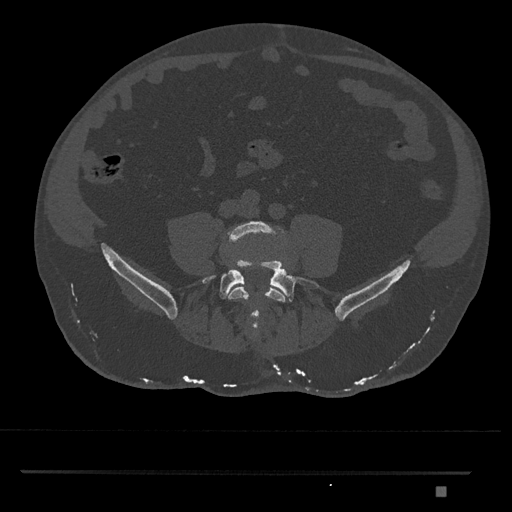
CT including the spine, one axial slice. Slice 579 of 1134 in the series (ordered by position). 120 kVp. Bone window (W 1800 / L 400 HU). 0.5 mm slice thickness. 512 × 512 image matrix. Male patient, age 65 years. Case-level facts recorded for this patient, not image findings: primary cancer: prostate.
Annotated regions visible in this slice (semi-automatic segmentation, software-assisted and operator-edited):
- L4 vertebra: box from (x=226, y=221) to (x=286, y=325) px
- L5 vertebra: (x=203, y=260)–(x=322, y=327)